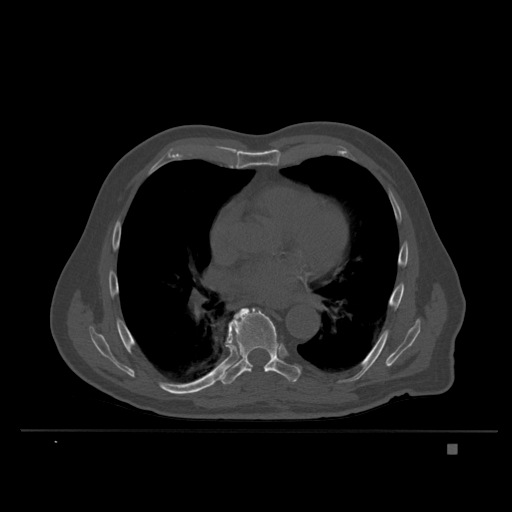
CT including the spine, one axial slice; slice 233 of 435 in the series (ordered by position); bone window (W 1800 / L 400 HU); 1.5 mm slice thickness; 512 × 512 image matrix, field of view 434 × 434 mm. Patient: male, 73 years. Case-level facts recorded for this patient, not image findings: primary cancer: skin.
Outlined on this slice (semi-automatic segmentation, software-assisted and operator-edited):
- T7 vertebra: box from (x=227, y=321) to (x=233, y=342) px
- T8 vertebra: (x=219, y=308)–(x=300, y=385)